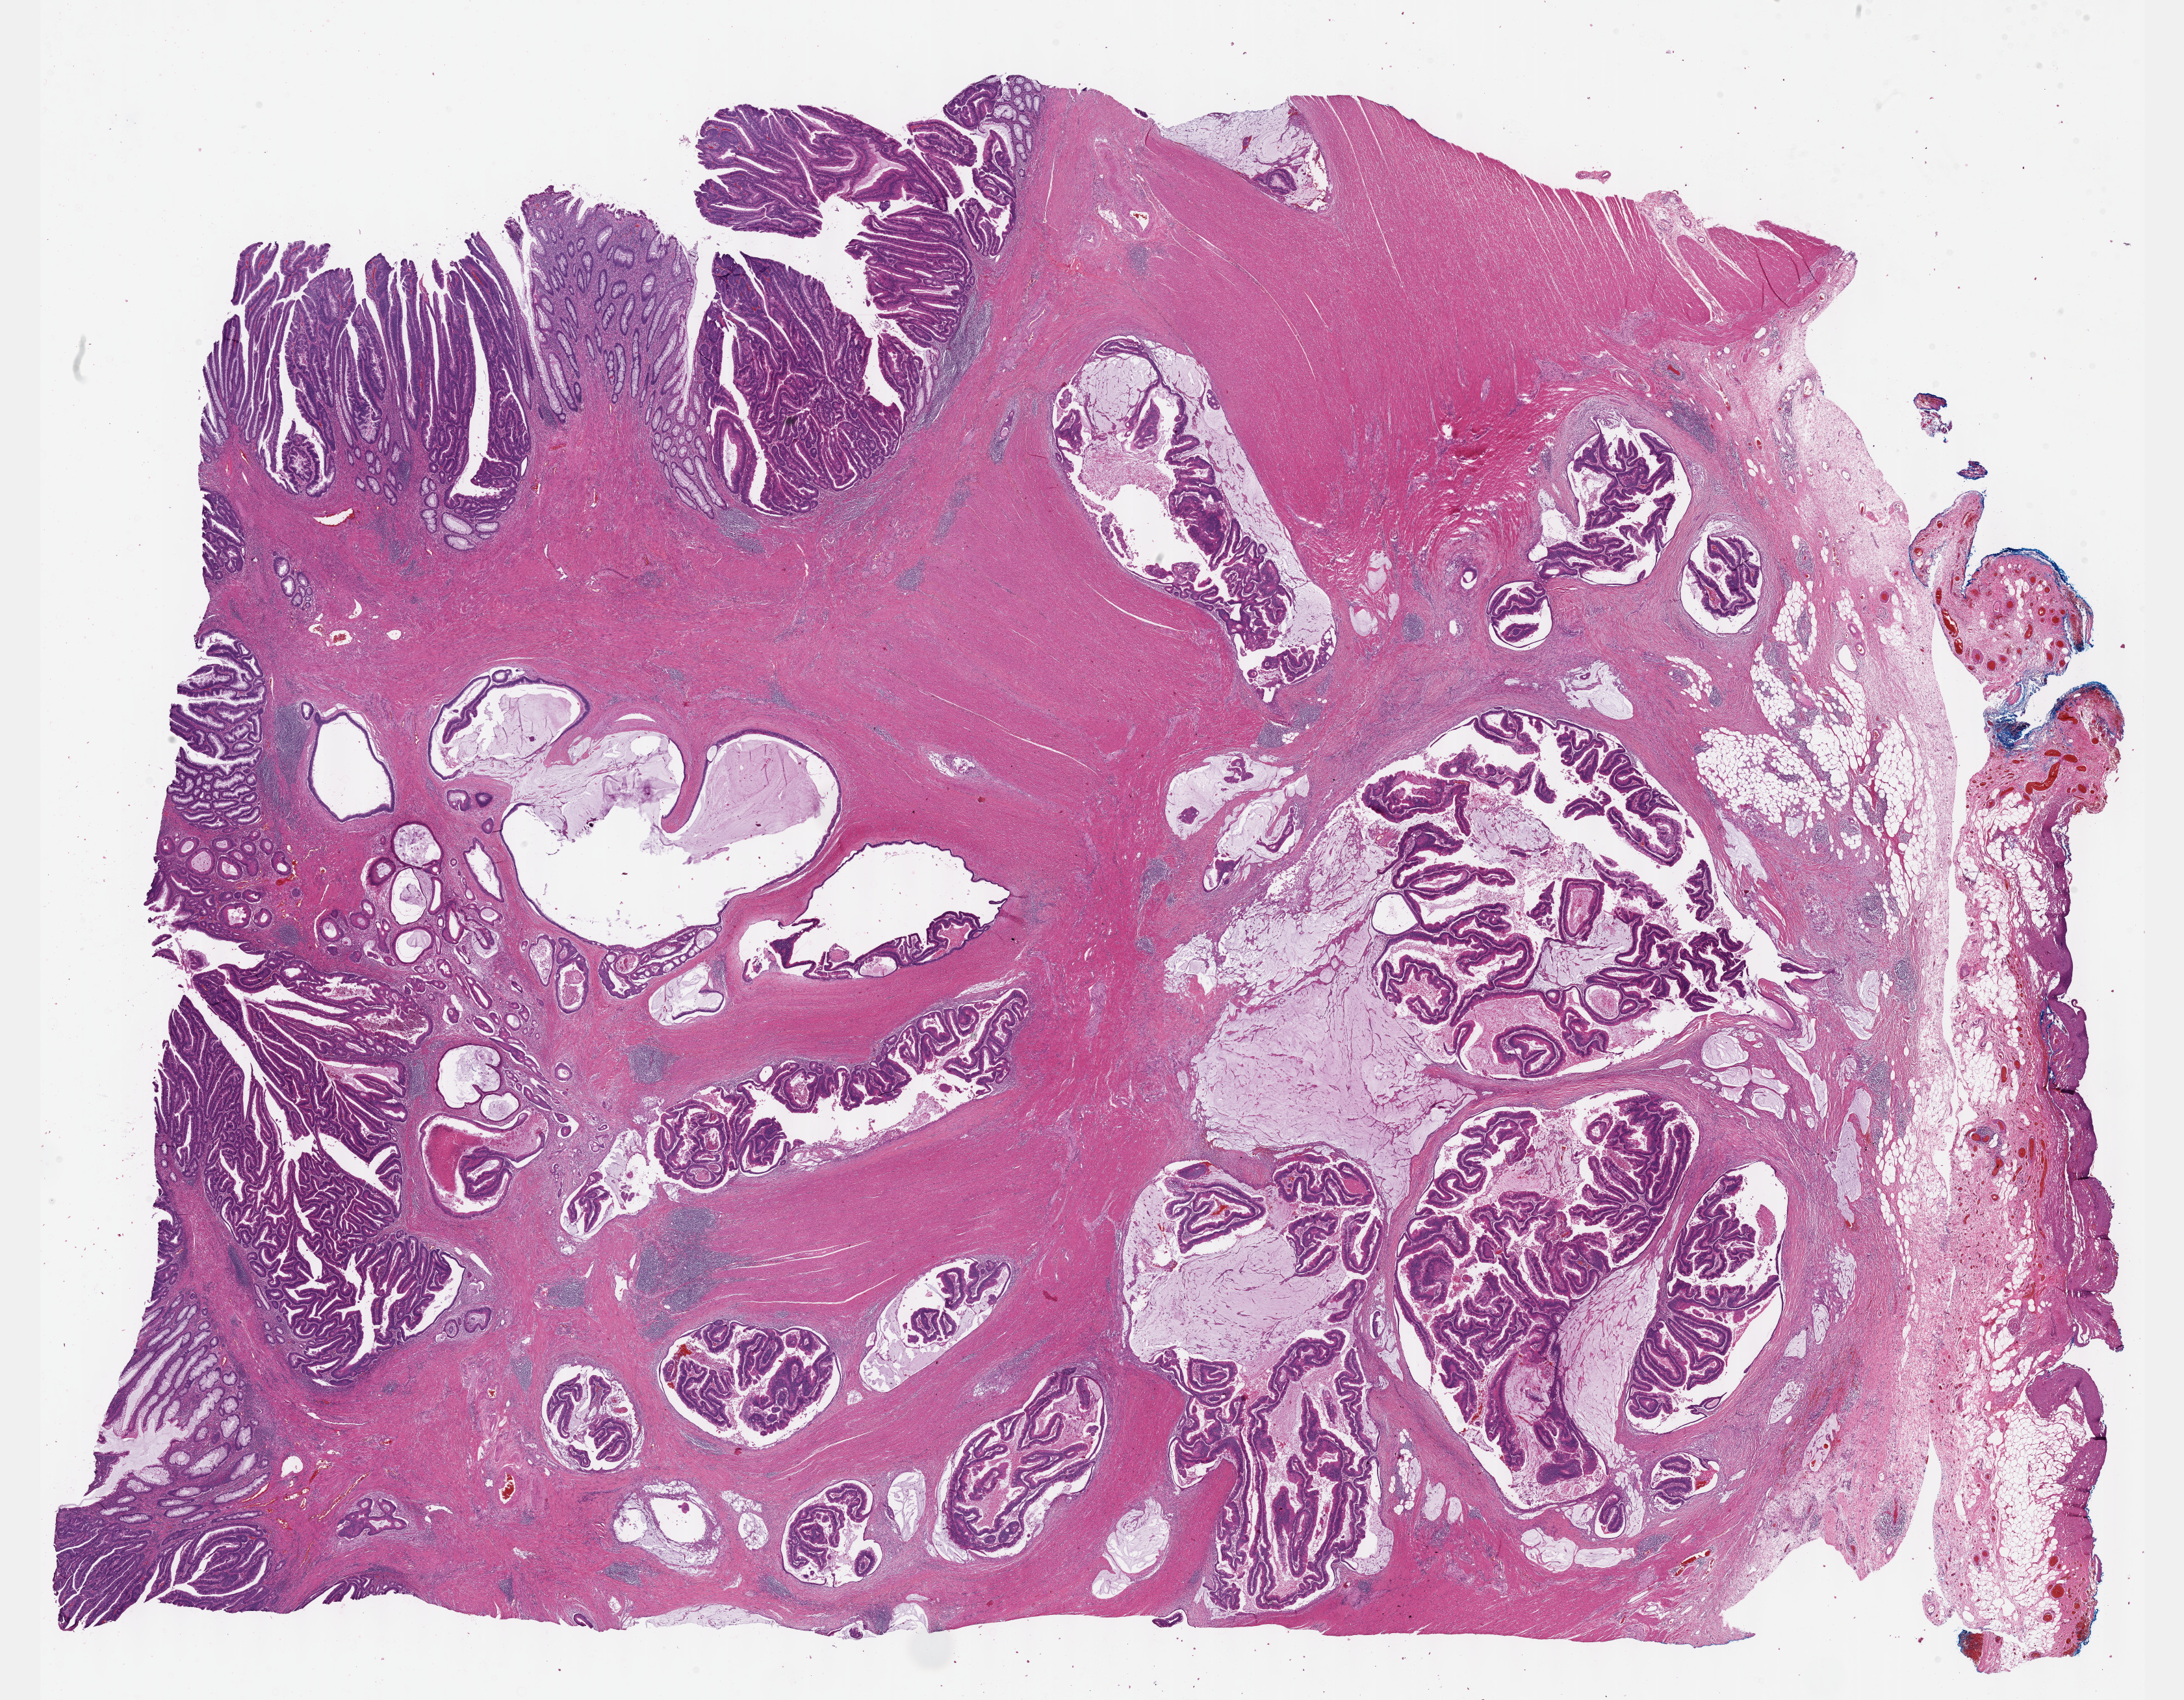
Digitized Hematoxylin and eosin (H&E) stained tissue section (whole slide), whole scanned area (about 27.2 x 21.1 mm) shown as a low-resolution overview. FFPE section. Colon, primary tumour sample. Female patient; age at initial diagnosis 42 years.
AJCC pathologic stage: IIA (7th edition). Lymph nodes positive (case pathology): 0 of 24 examined. Diagnosis: Mucinous adenocarcinoma. TNM: T3 N0 MX.